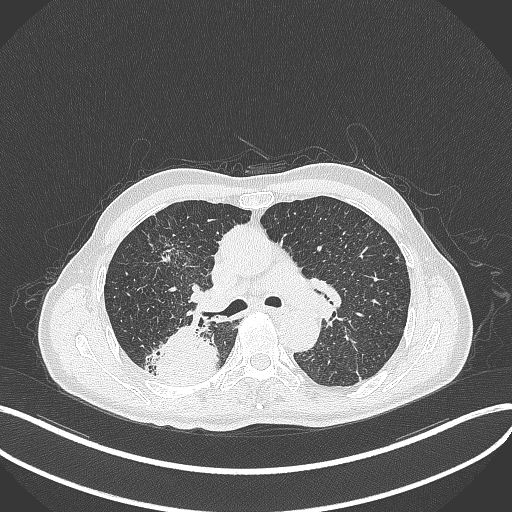
Chest CT, one axial slice. Position 289 of 428 along the scan axis. Lung window (W 1500 / L -600 HU). 1 mm slice thickness. 512 × 512 image matrix, field of view 400 × 400 mm. Patient: male, 79 years. From the clinical record (not read from this slice): clinical TNM (as recorded): T3 N0 M0.
Annotated regions visible in this slice (rectangle marked by the reading radiologist):
- lung tumour (recorded histology: adenocarcinoma): bounding box <148,326,219,385> (left, top, right, bottom; pixels)